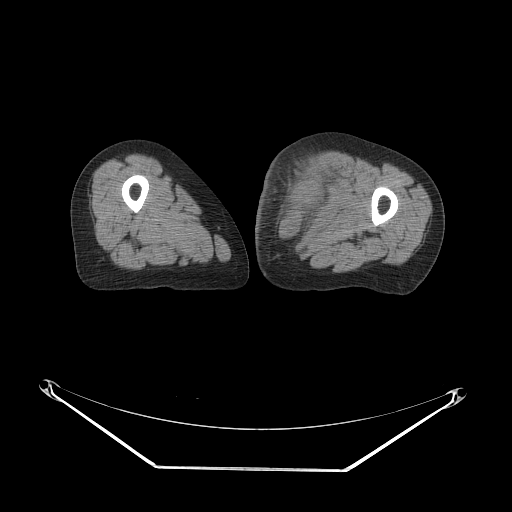
CT of an extremity soft-tissue mass (from a PET/CT study), one axial slice. Position 42 of 91 along the scan axis. 140 kVp. Soft-tissue window (W 400 / L 40 HU). 3.75 mm slice thickness. 512 × 512 image matrix, field of view 500 × 500 mm. Female patient. From the clinical record (not read from this slice): histological type: pleomorphic leiomyosarcoma; grade: high; site of the primary tumour: left thigh.
Outlined on this slice (expert contour drawn on MRI and transferred to this co-registered scan by the dataset authors):
- gross tumour volume including surrounding oedema: bounding box [x1, y1, x2, y2] px = [265, 148, 344, 236]
- gross tumour volume (mass): [279, 148, 334, 225]